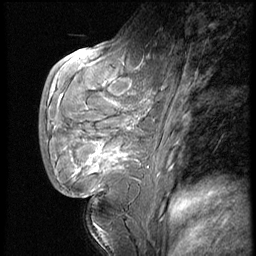
Breast MRI (dynamic contrast-enhanced), one sagittal slice. Slice 20 of 62 in the series (ordered by position). Dynamic contrast-enhanced series, image 2 of 4 at this slice position (ordered by acquisition). 1.5 T. TE 4.2 ms, TR 9 ms. 2.5 mm slice thickness. 256 × 256 image matrix, field of view 180 × 180 mm. Female patient, age 28 years. Case-level facts recorded for this patient, not image findings: setting: breast cancer imaged before/during neoadjuvant chemotherapy.
Structures marked on this image (semi-automatic segmentation, software-assisted and operator-edited):
- analysis volume of interest (the breast-tissue region the enhancement analysis was run in; not a lesion): box from (x=45, y=54) to (x=150, y=183) px
- tumour enhancement mask (voxels above the 140 % enhancement threshold inside the analysis volume of interest): (x=80, y=141)–(x=128, y=172)